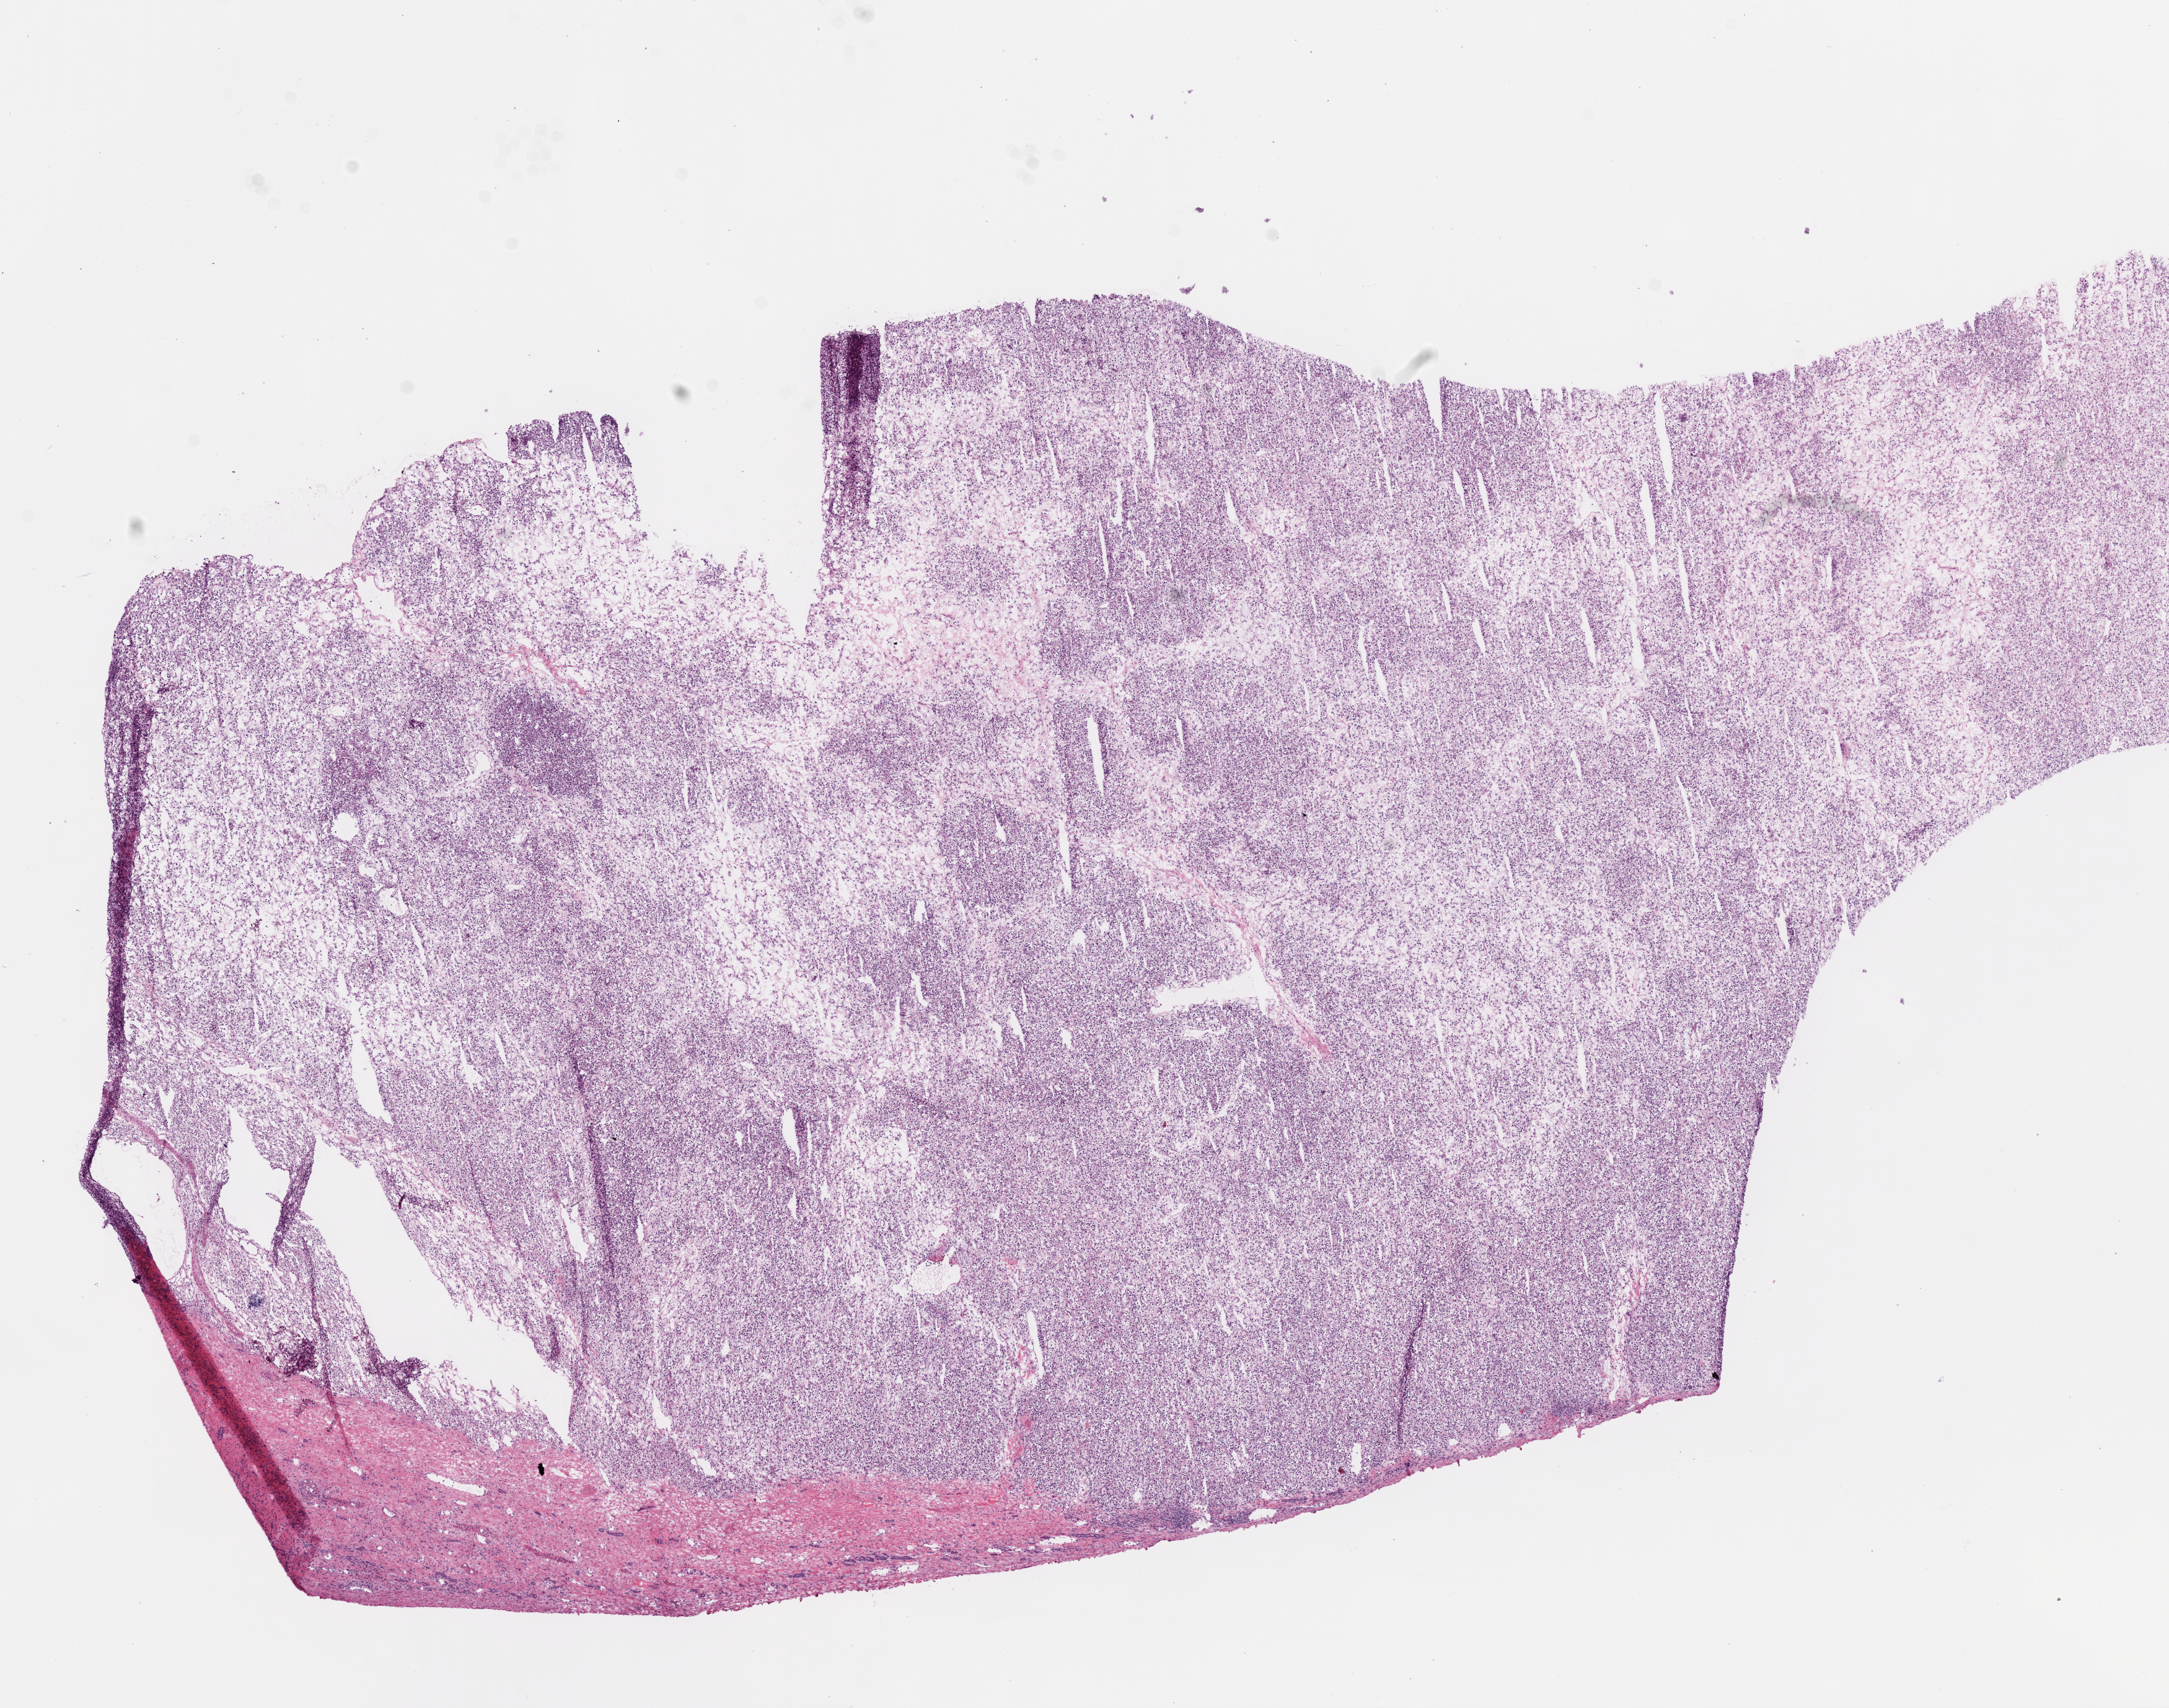
Whole-slide histology image, H&E — low-resolution overview of the scanned area, about 14.0 x 11.1 mm. Frozen section. Sample: primary tumour, kidney. Male patient; age at initial diagnosis 52 years.
Diagnosis: Clear cell adenocarcinoma, NOS.